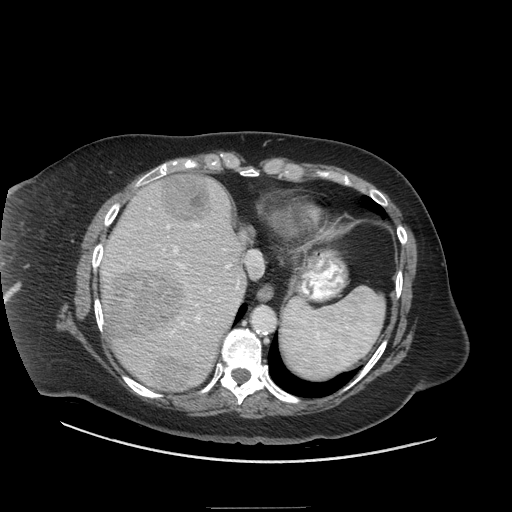
Contrast-enhanced abdominal CT (liver protocol), one axial slice; slice 53 of 81 in the series (ordered by position); reconstruction kernel STANDARD; soft-tissue window (W 400 / L 40 HU); 512 × 512 image matrix. From the clinical record (not read from this slice): diagnosis: hepatocellular carcinoma (patient treated with transarterial chemoembolisation; whether this scan precedes or follows treatment is not stated here); TNM stage (as recorded): Stage-II; Child-Pugh class: A; tumour differentiation: moderately differentiated; tumour nodularity: multinodular.
Outlined on this slice (semi-automatically segmented with operator editing):
- liver parenchyma outside the tumour (the mass and vessels are separate outlines, so this box may not span the whole liver): bounding box <100,176,246,392> (left, top, right, bottom; pixels)
- mass: <110,172,212,389>
- liver vessels: <102,208,240,372>